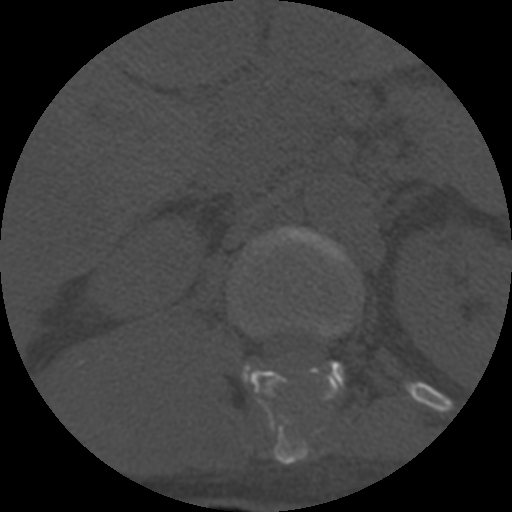
CT including the spine, one axial slice. Slice 302 of 708 in the series (ordered by position). Reconstruction kernel STANDARD. 120 kVp. One of 3 acquisitions stored at this slice position. Bone window (W 1800 / L 400 HU). 1.25 mm slice thickness. 512 × 512 image matrix, field of view 160 × 160 mm. Patient age 55 years. From the clinical record (not read from this slice): primary cancer: colon; vertebrae with lytic lesions (as recorded): T12, L1, L5.
Outlined on this slice (semi-automatic segmentation, software-assisted and operator-edited):
- L1 vertebra: bounding box <243,227,346,399> (left, top, right, bottom; pixels)
- T12 vertebra: <251,323,333,465>